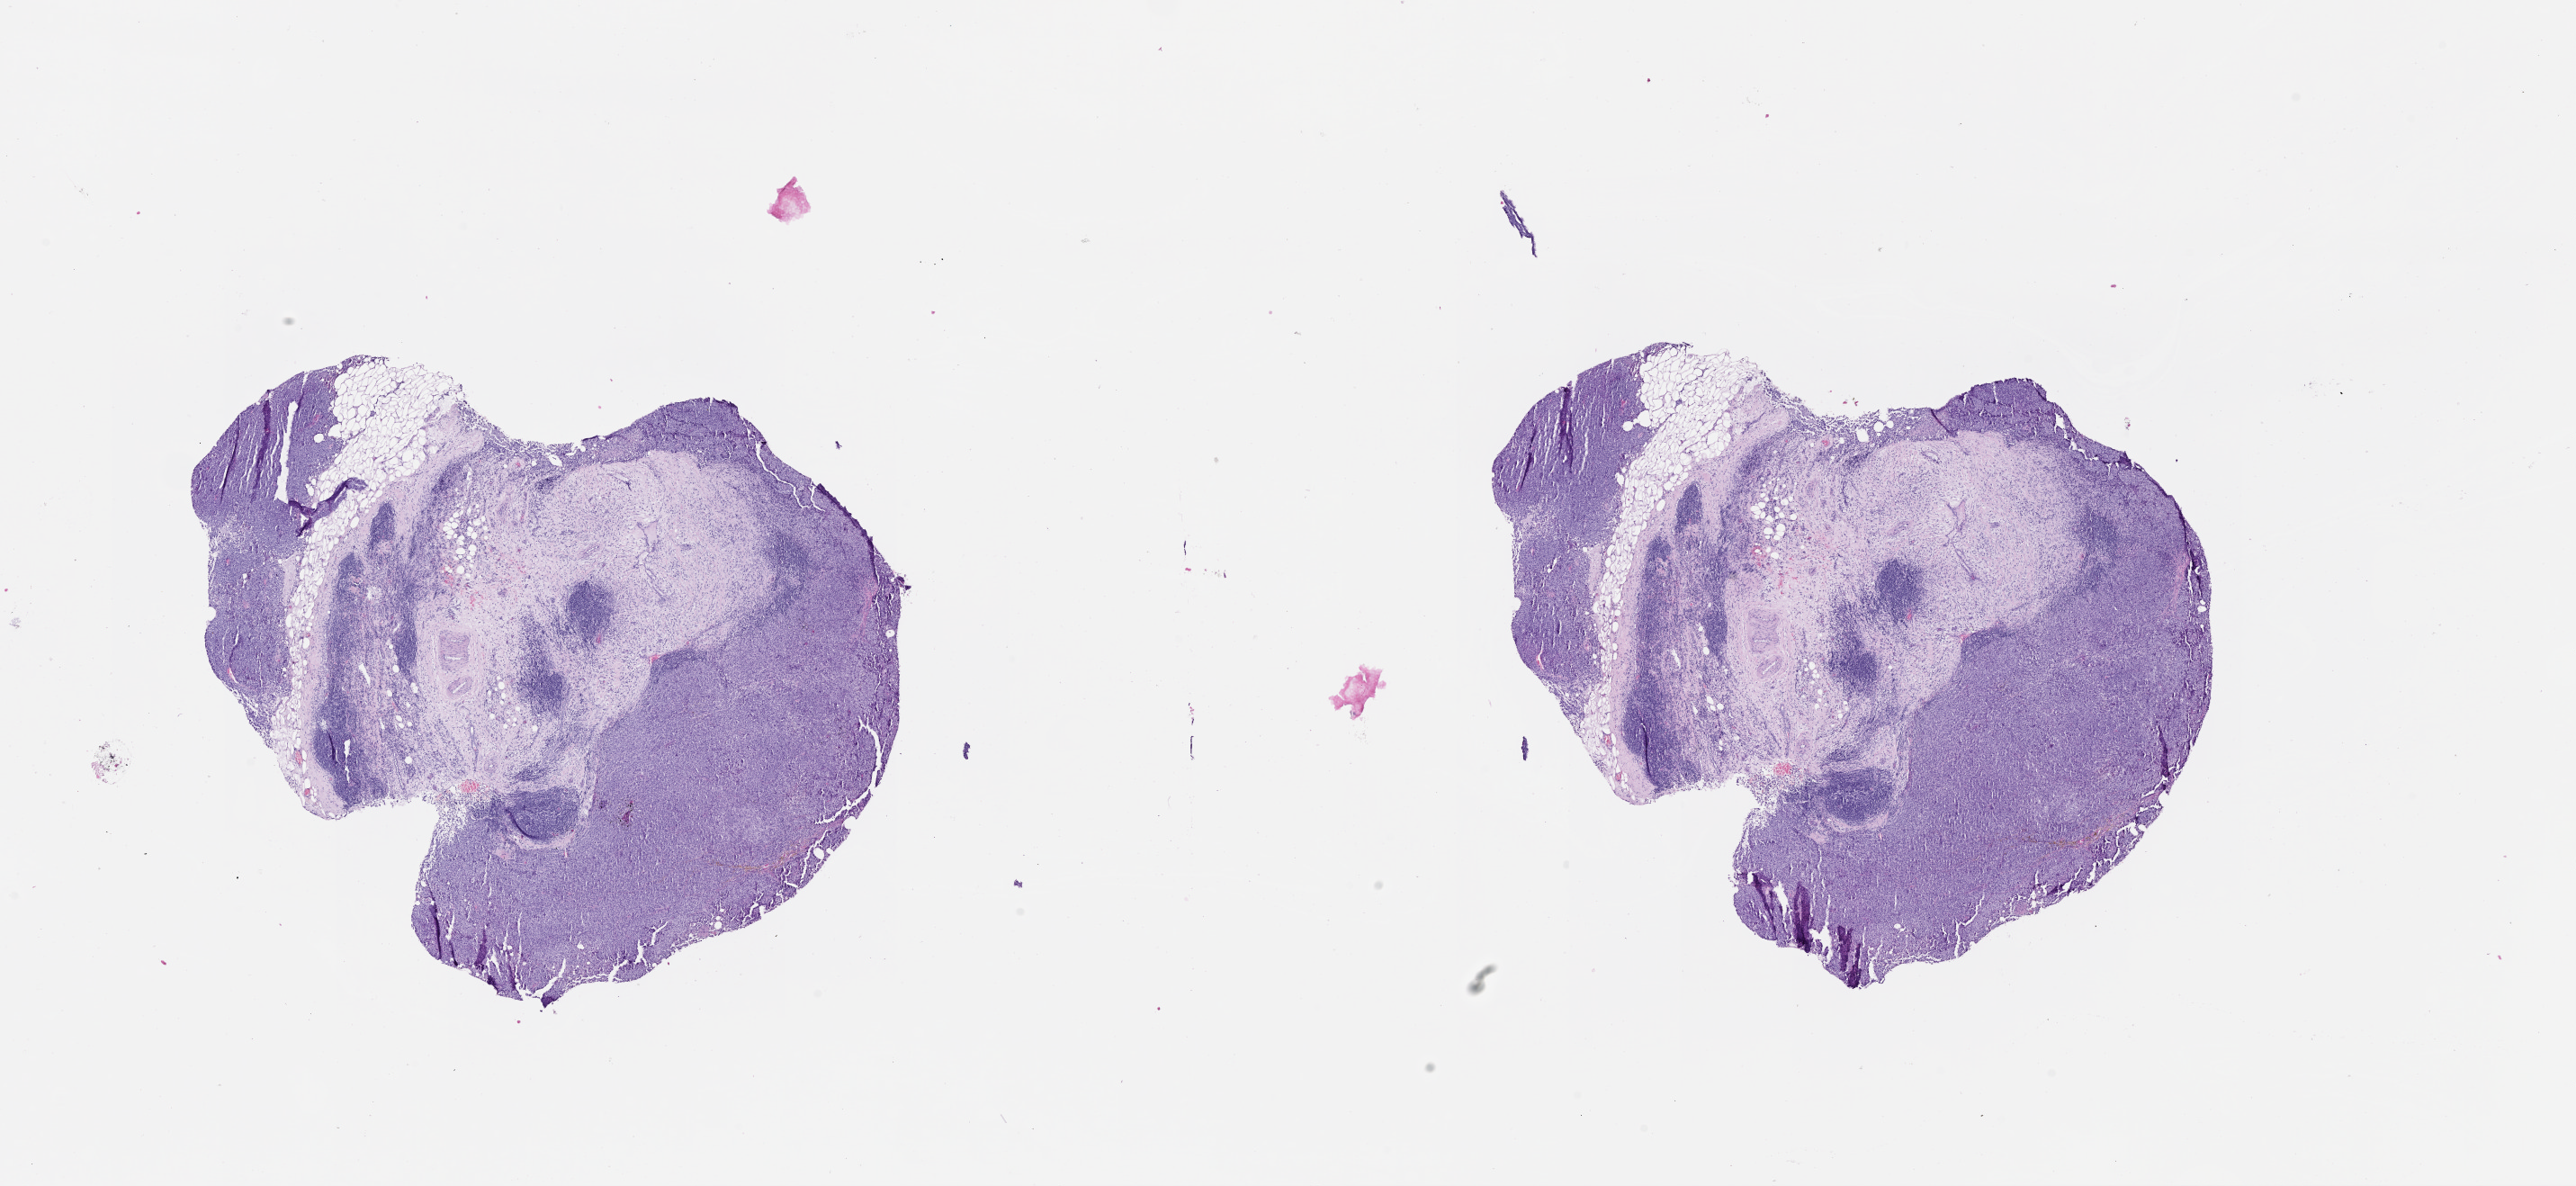
Digitized Hematoxylin and eosin (H&E) stained tissue section (whole slide), a low-resolution overview of the entire scanned area, about 23.1 x 10.6 mm. Tumour tissue sample, sampled site: lymph node. Male, 72 y/o. Composition of this section per pathologist review: tumour nuclei 30%, necrosis 0%.
This section: metastatic tumour tissue. Patient diagnosis: Malignant melanoma, NOS.